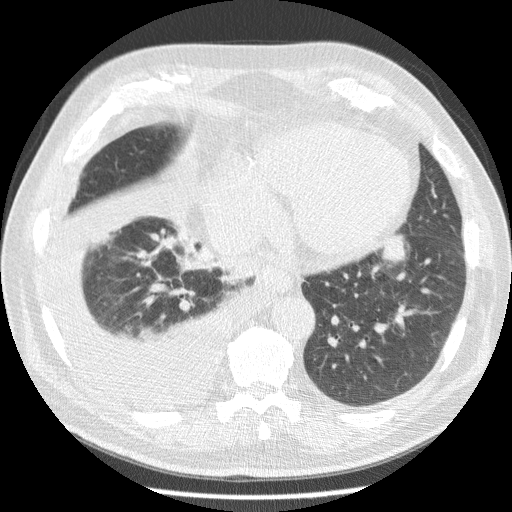
Chest CT (low-dose screening protocol), one axial image. Third annual screen. Lung window (W 1500 / L -600 HU). Standard (soft-tissue) reconstruction kernel (STANDARD). Male participant, aged 63 years at enrolment. Current smoker at enrolment.
Expert-annotated lung lesion, bounding box <348,226,416,298> (left, top, right, bottom; pixels). Reader record for this screening exam (exam-level; its link to the box is not recorded): non-calcified nodule or mass ≥4 mm, left lower lobe, 34 × 31 mm, smooth margins, soft tissue attenuation, pre-existing on the prior screen: yes; interval growth: yes. Participant outcome: lung cancer diagnosed 30 days after this screen — squamous cell carcinoma, NOS, left lower lobe, stage IB (AJCC 6th edition), 48 mm at pathology.